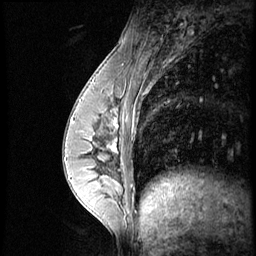
Breast MRI (dynamic contrast-enhanced), one sagittal slice. Position 21 of 56 along the scan axis. Dynamic contrast-enhanced series, image 2 of 4 at this slice position (ordered by acquisition). 1.5 T. TE 4.2 ms, TR 8.9 ms. 2.5 mm slice thickness. 256 × 256 image matrix. Patient: female, 35 years. Case-level facts recorded for this patient, not image findings: setting: breast cancer imaged before/during neoadjuvant chemotherapy; receptor status: HER2-positive.
Outlined on this slice (semi-automatic segmentation, software-assisted and operator-edited):
- analysis volume of interest (the breast-tissue region the enhancement analysis was run in; not a lesion): box from (x=73, y=111) to (x=131, y=164) px
- tumour enhancement mask (voxels above the 140 % enhancement threshold inside the analysis volume of interest): (x=73, y=111)–(x=118, y=152)